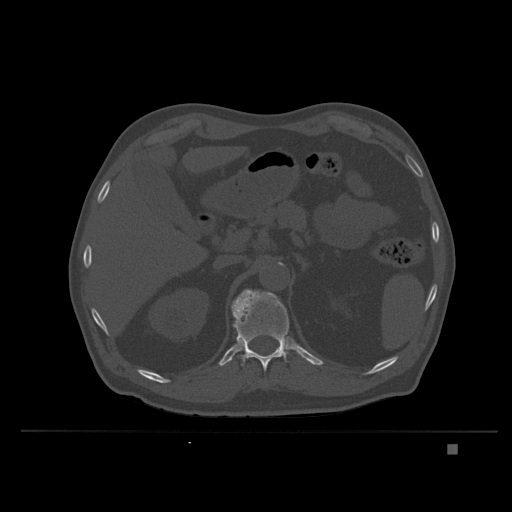
CT including the spine, one axial slice; position 158 of 435 along the scan axis; bone window (W 1800 / L 400 HU); 512 × 512 image matrix. Patient: male, 73 years. Case-level facts recorded for this patient, not image findings: primary cancer: skin.
Structures marked on this image (semi-automatically segmented with operator editing):
- T12 vertebra: bounding box (x1, y1, x2, y2) in pixels: (231, 289, 289, 385)